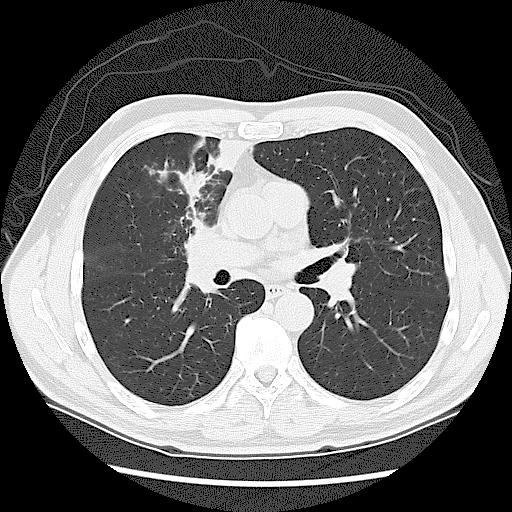
Axial slice from a low-dose chest CT screening exam. Baseline screening round. Lung window (W 1500 / L -600 HU). 2.5 mm slice thickness. Slice 62 of 131 in the series. Male participant, aged 60 years at enrolment. Current smoker at enrolment.
Expert reader's lesion annotation, box from (x=158, y=215) to (x=240, y=305) px. No non-calcified nodule or mass ≥4 mm was recorded by the screening reader at this exam. Official screen result: negative screen, significant abnormalities not suspicious for lung cancer. Participant outcome: lung cancer diagnosed 41 days after this screen — small cell carcinoma, NOS, right upper lobe, stage IIIA (AJCC 6th edition).